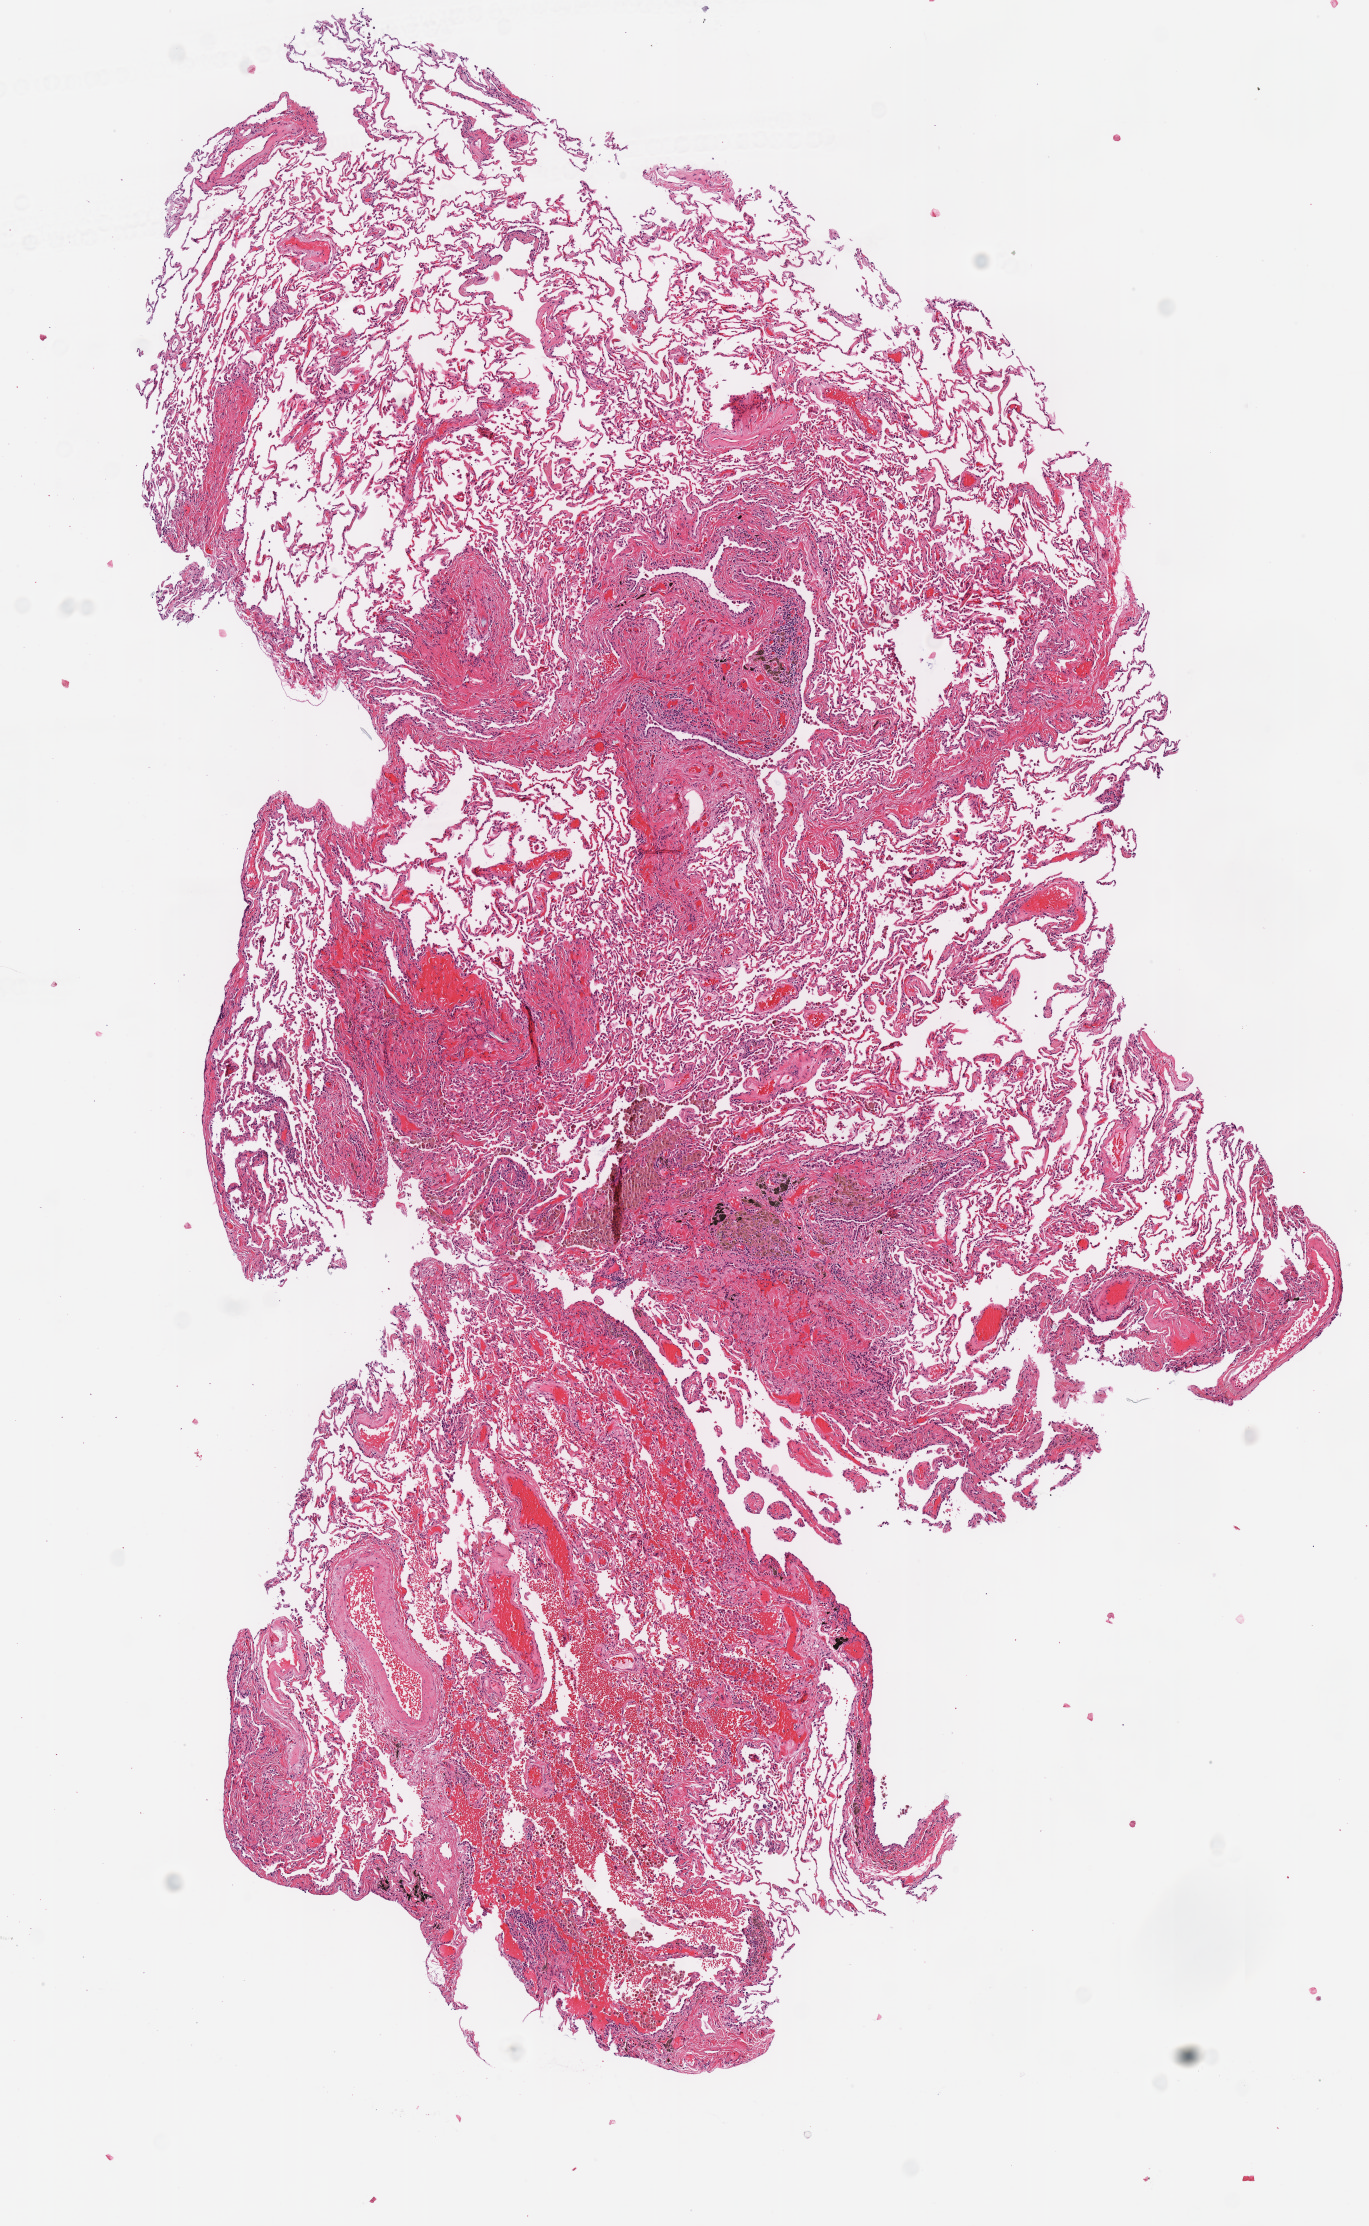
Whole-slide histology image, Hematoxylin and eosin (H&E) stained — whole scanned area (about 5.4 x 8.8 mm, from a 40x scan) shown as a low-resolution overview; frozen section from the top of the tissue portion; sample: solid tissue normal (non-tumour tissue), lung. Male, age 61 years at initial diagnosis.
• this section: solid tissue normal (non-tumour) sample from the same patient
• patient diagnosis: Adenocarcinoma, NOS (upper lobe, lung)